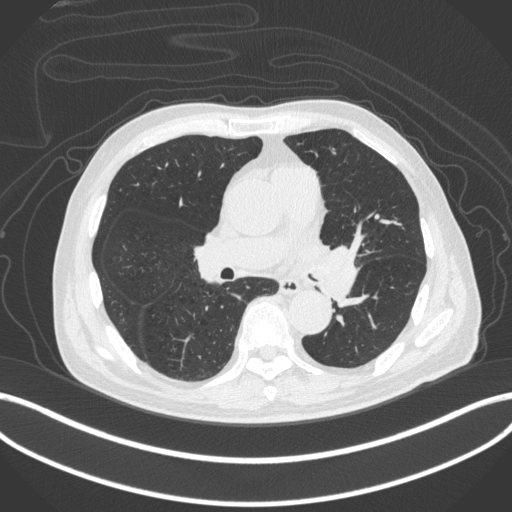
Chest CT, one axial slice. Position 233 of 420 along the scan axis. Reconstruction kernel B31f. Lung window (W 1500 / L -600 HU). 1 mm slice thickness. 512 × 512 image matrix, field of view 400 × 400 mm. Male patient, age 77 years. Case-level facts recorded for this patient, not image findings: clinical TNM (as recorded): T3 N1 M0.
Structures marked on this image (rectangle marked by the reading radiologist):
- lung tumour (recorded histology: adenocarcinoma): bounding box (x1, y1, x2, y2) in pixels: (313, 240, 362, 308)